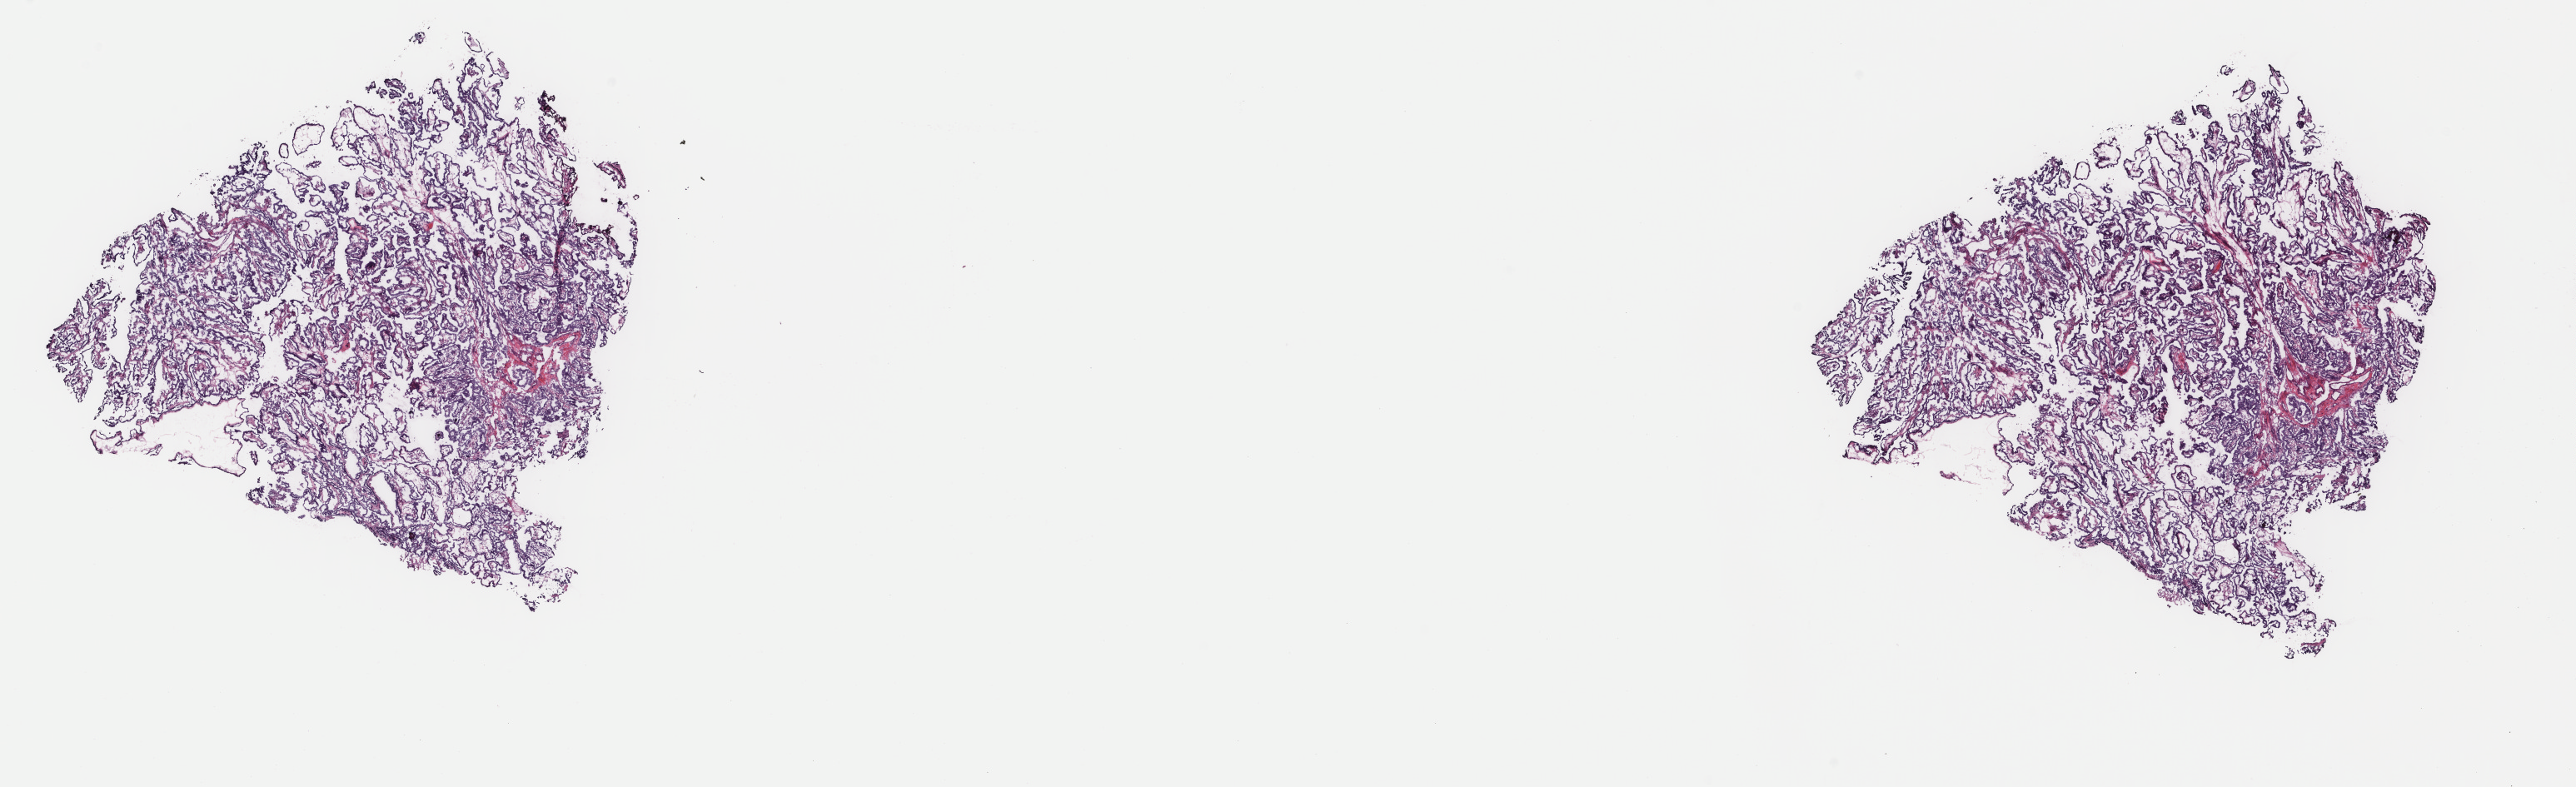
Digitized H&E tissue section (whole slide), shown as a low-resolution overview of the whole scanned area (about 24.6 x 7.5 mm), frozen section from the top of the tissue portion, primary tumour sample from the thyroid. Female patient; age at initial diagnosis 23 years. Pathologist review of this section (percent, as recorded): tumour cells 100%, tumour nuclei 95%, normal cells 0%, stromal cells 0%, necrosis 0%. Inflammatory infiltration, as recorded: lymphocyte infiltration 0%, monocyte infiltration 0%, neutrophil infiltration 0%.
AJCC pathologic stage: I (6th edition). TNM: T2 NX MX. Histologic diagnosis: Papillary adenocarcinoma, NOS.